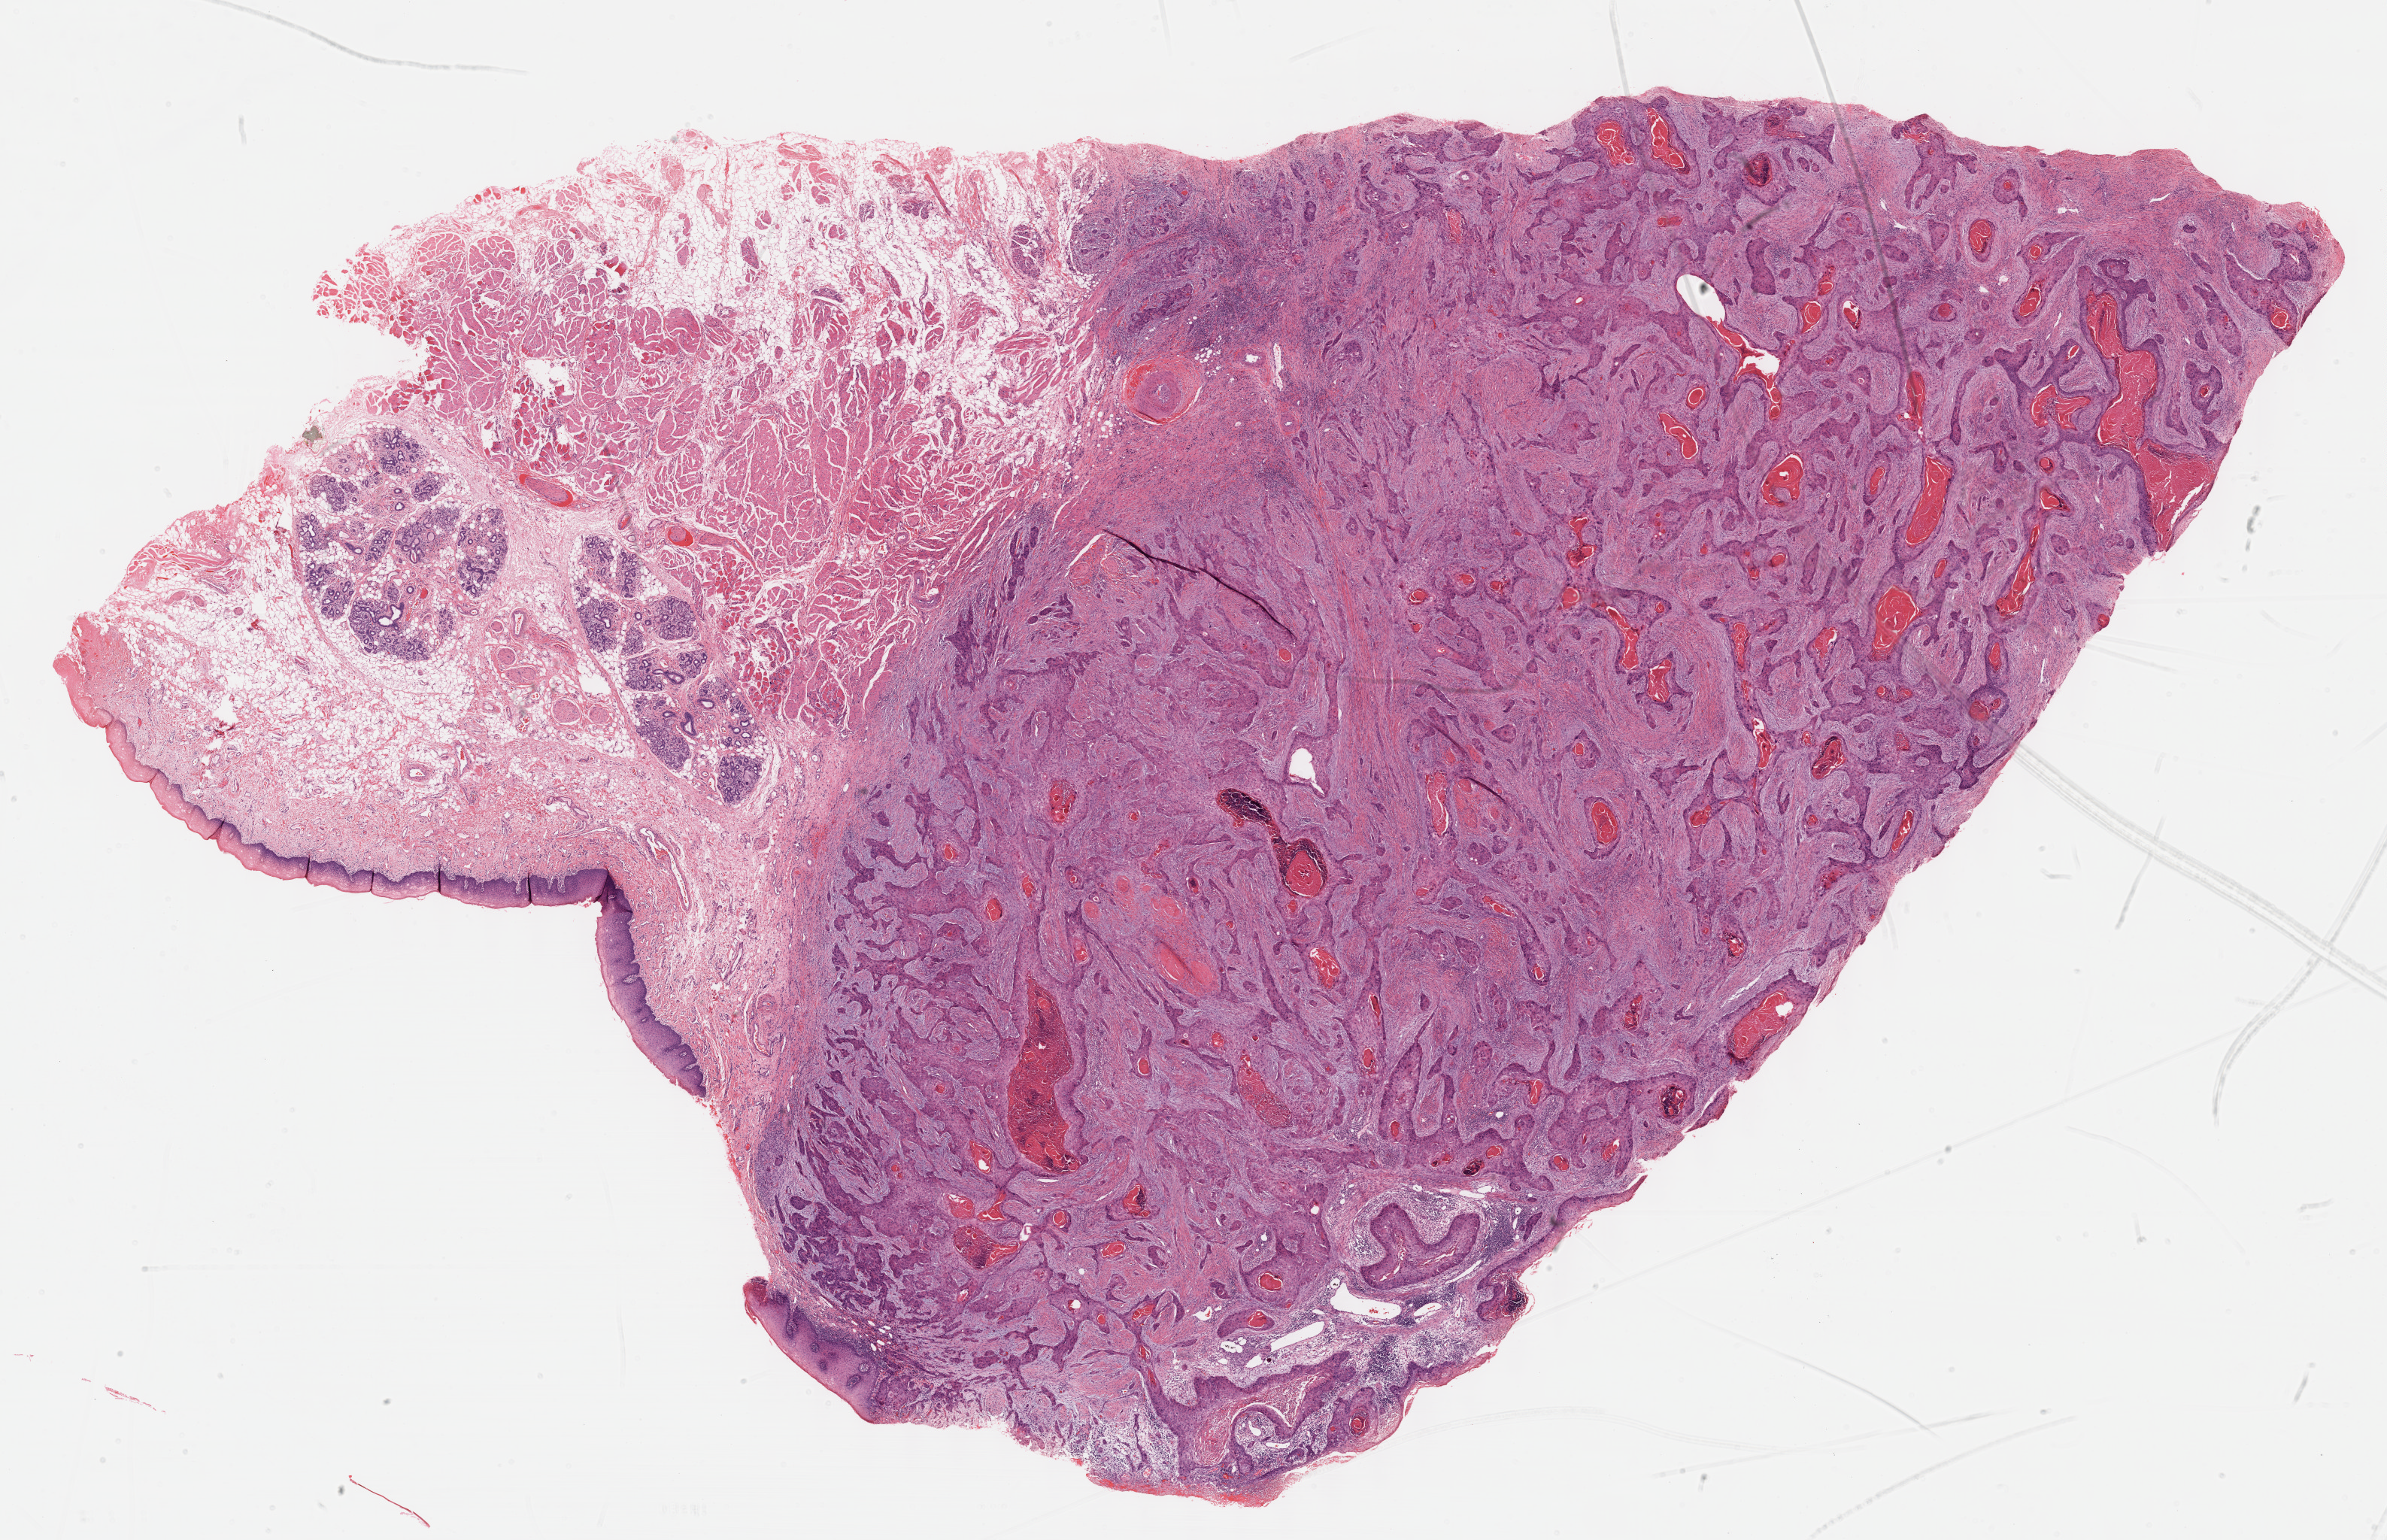
Digitized H&E-stained tissue section (whole slide), whole scanned area (about 25.7 x 16.6 mm, from a 40x scan) shown as a low-resolution overview; formalin-fixed paraffin-embedded (FFPE) diagnostic section; primary tumour sample from the head and neck. Male patient; age at initial diagnosis 71 years. Histologic grade: G2 (moderately differentiated).
- AJCC pathologic stage: II
- pathologic diagnosis: Squamous cell carcinoma, NOS (overlapping lesion of lip, oral cavity and pharynx)
- TNM: T2 N0